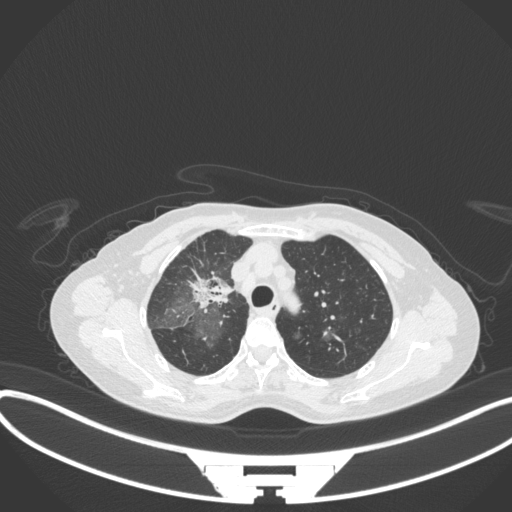
Chest CT, one axial slice; slice 243 of 311 in the series (ordered by position); lung window (W 1500 / L -600 HU); 1 mm slice thickness; 512 × 512 image matrix. Patient: female, 59 years. From the clinical record (not read from this slice): clinical TNM (as recorded): T3 N0 M0.
Outlined on this slice (bounding box drawn by a radiologist):
- lung tumour (recorded histology: adenocarcinoma): bounding box [x1, y1, x2, y2] px = [186, 265, 235, 312]